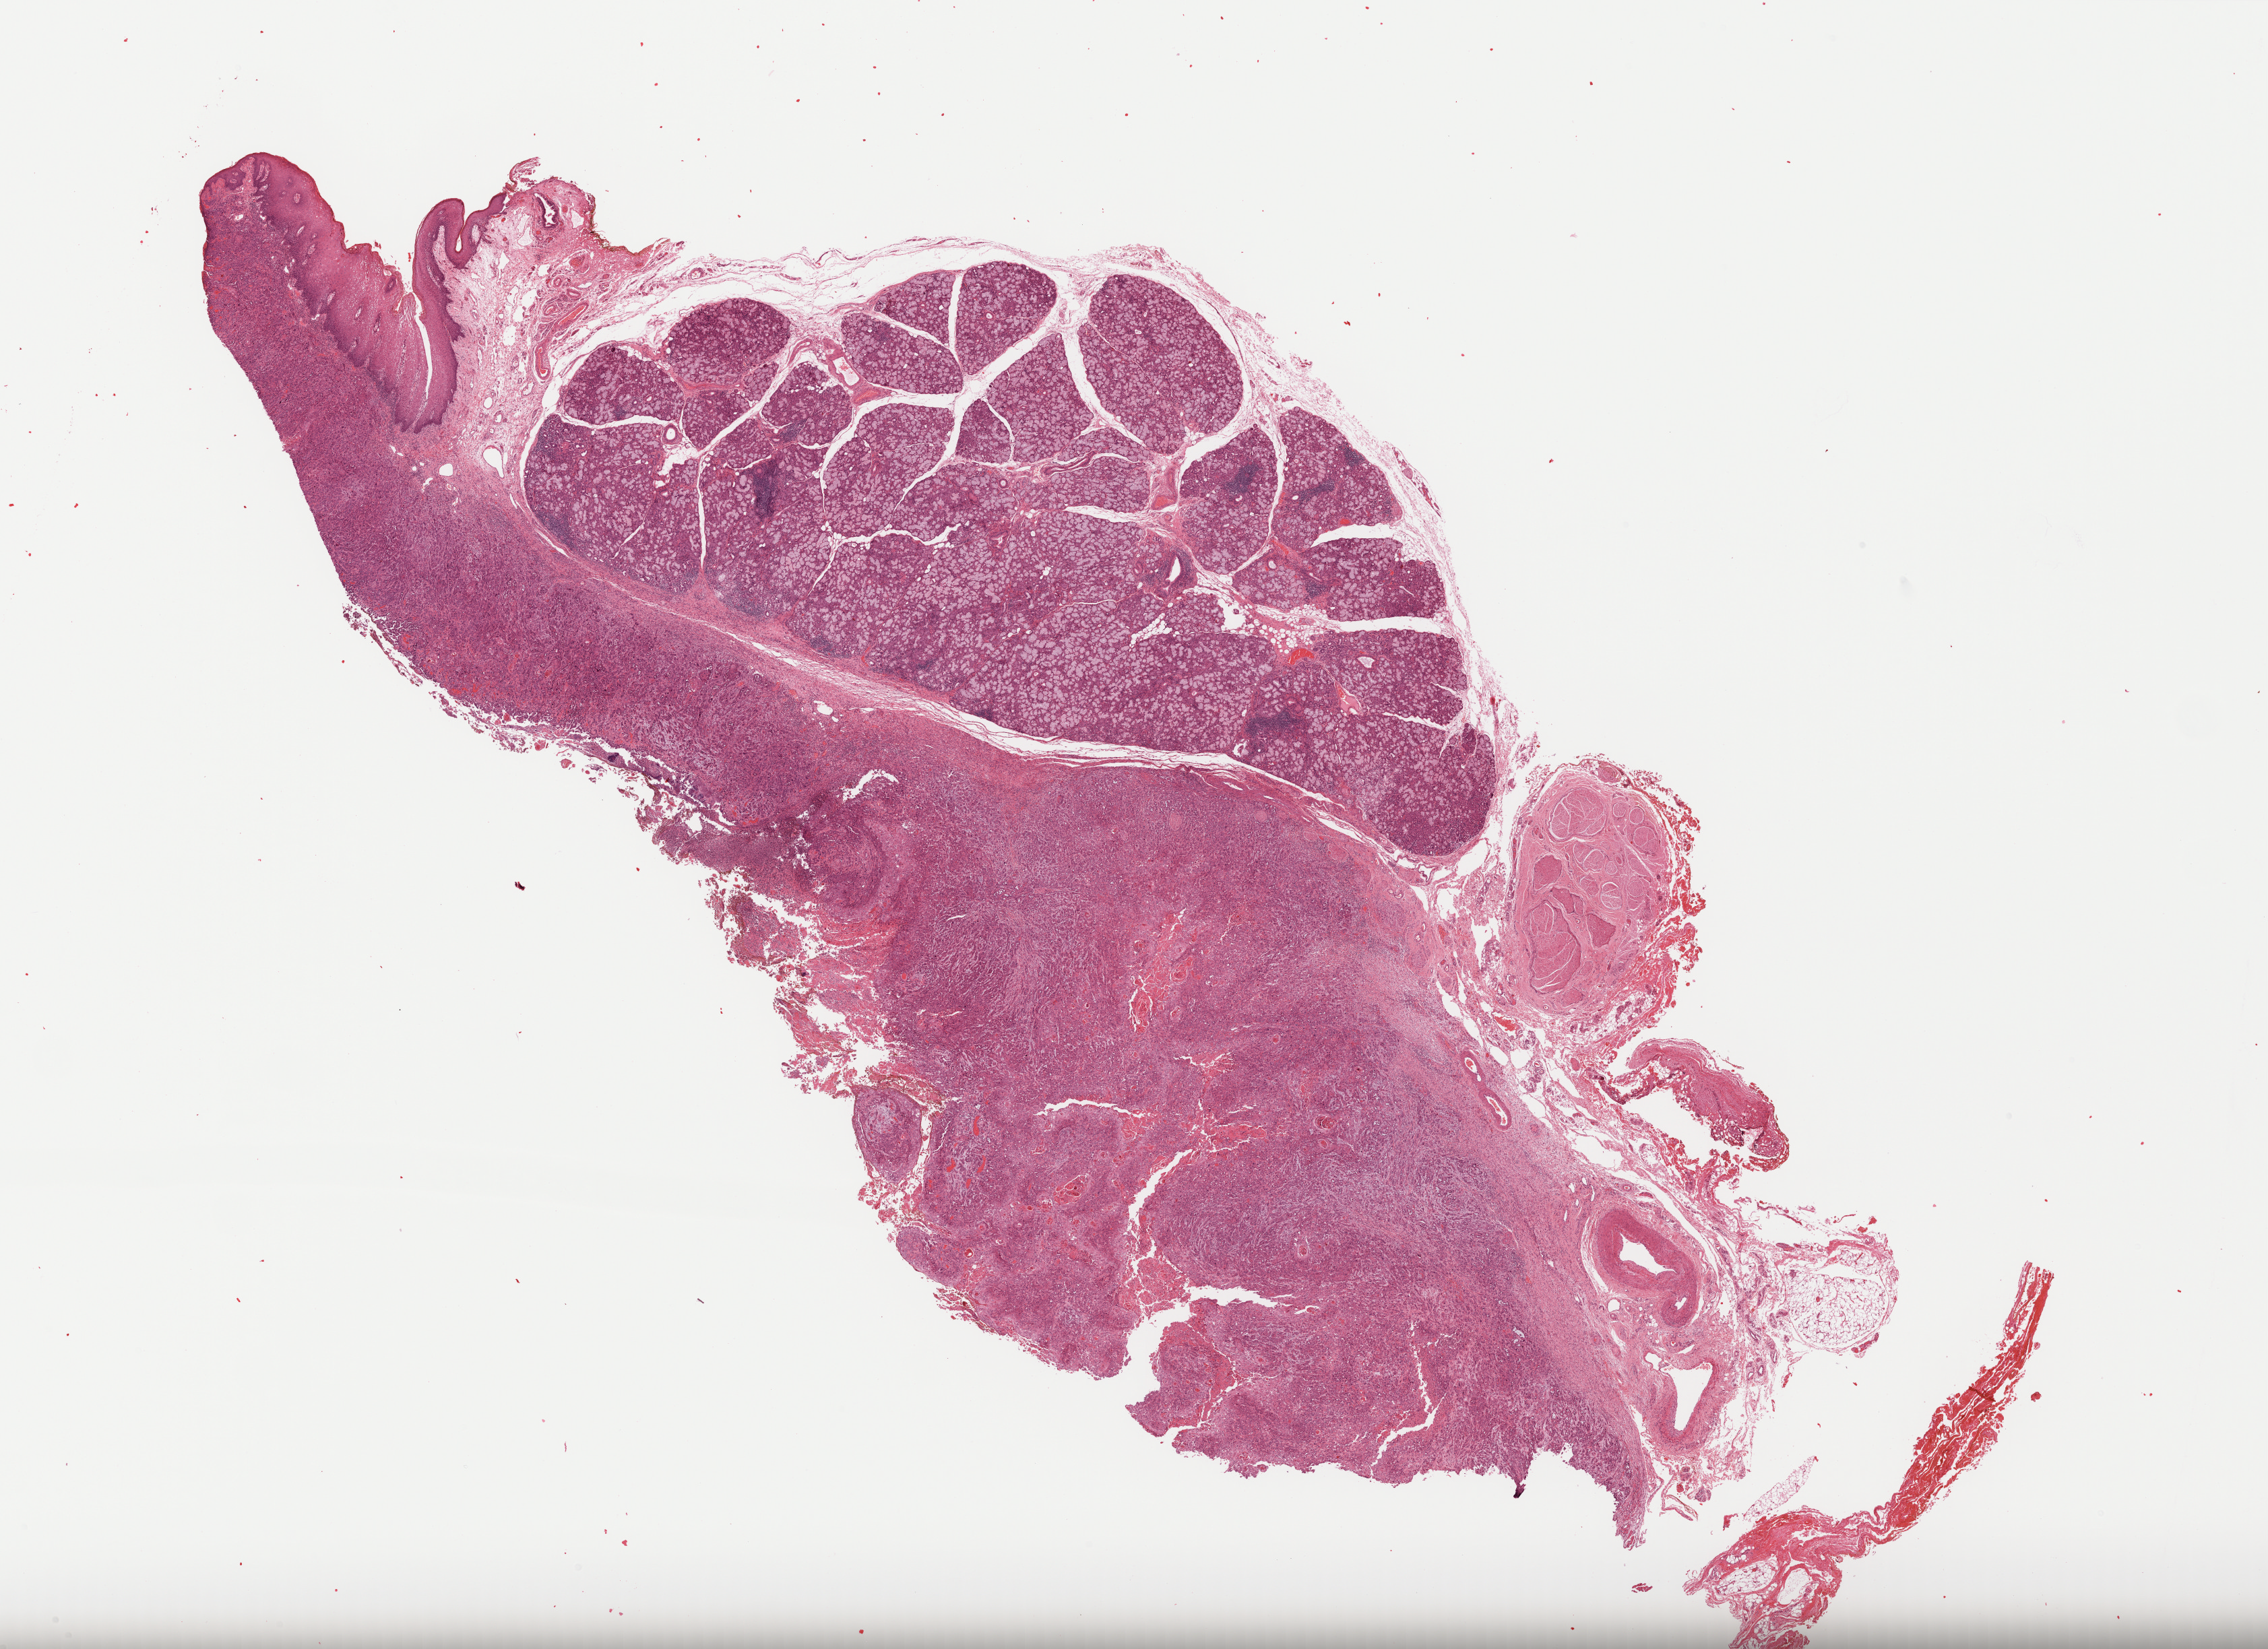
Digitized Hematoxylin and eosin (H&E) stained tissue section (whole slide) — a low-resolution overview of the entire scanned area, about 27.1 x 19.7 mm (acquisition: 40x scan). FFPE section. Sample: primary tumour, head and neck. Male, age 67 years at initial diagnosis. Histologic grade: G3 (poorly differentiated).
TNM: T4a N2c. AJCC pathologic stage: IVA. Pathologic diagnosis: Squamous cell carcinoma, NOS (overlapping lesion of lip, oral cavity and pharynx). Laterality: right.